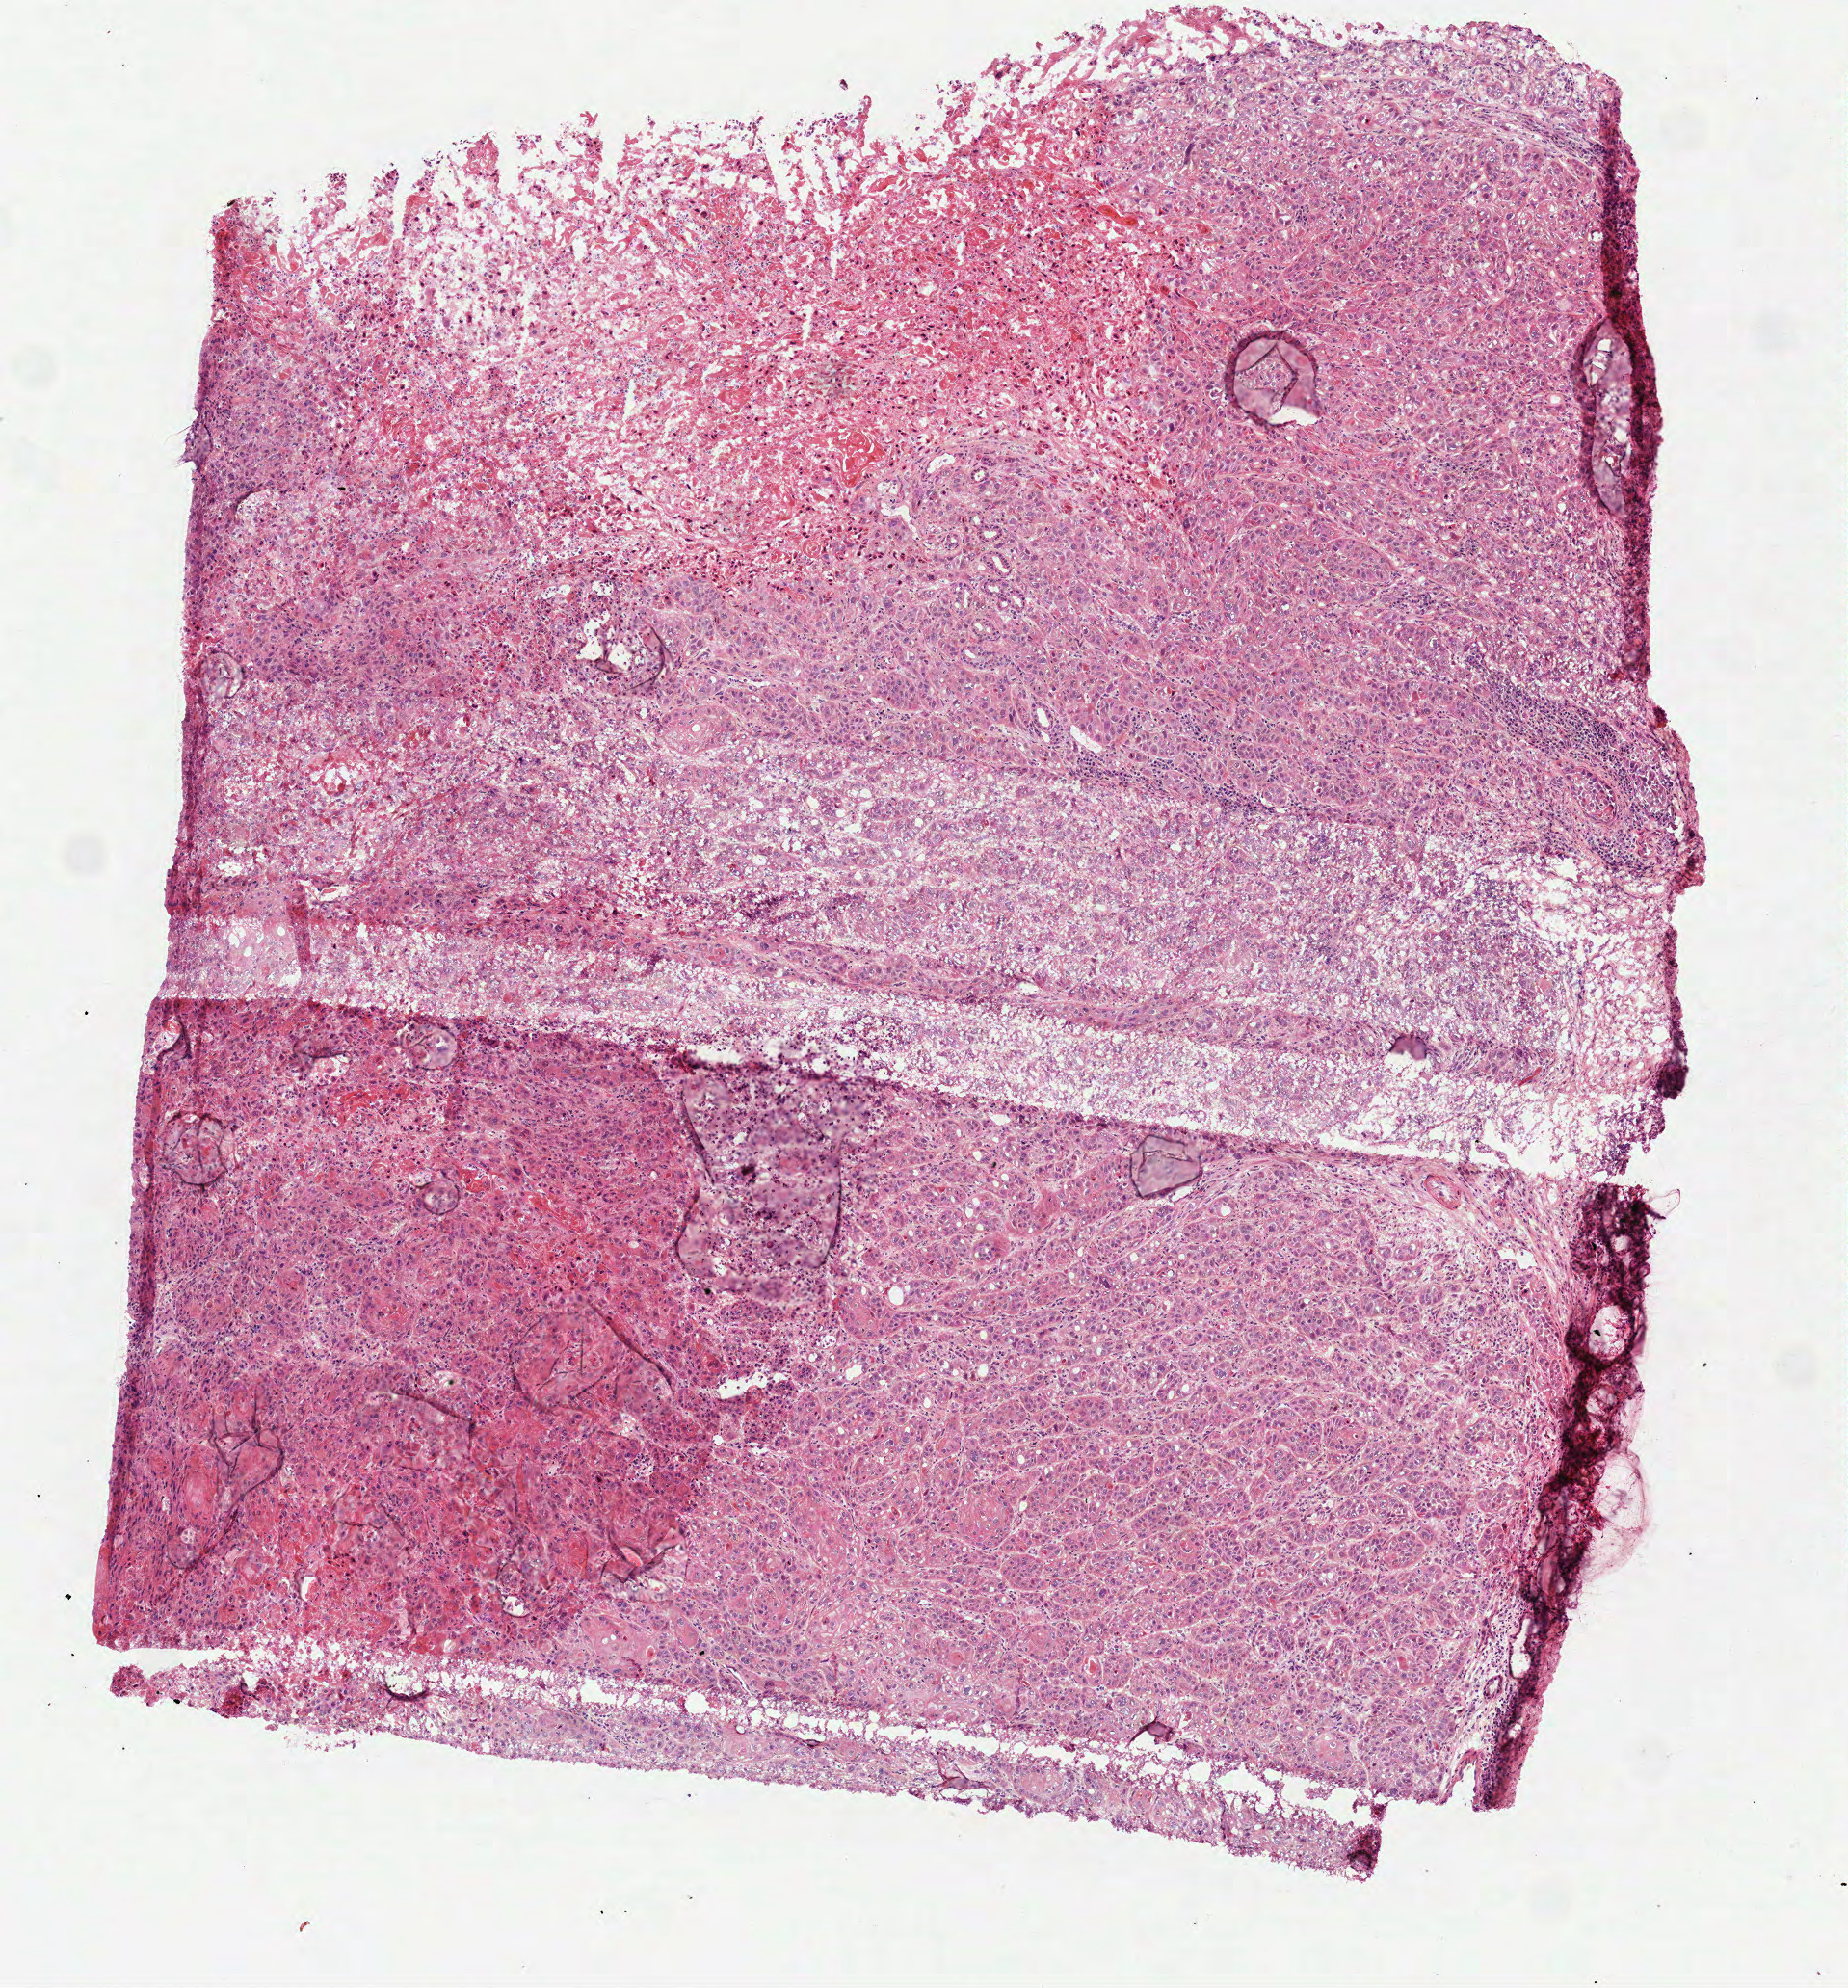
Whole-slide histology image, H&E-stained, low-resolution overview of the scanned area, about 3.9 x 4.2 mm (from a 40x scan). Frozen section from the top of the tissue portion. Primary tumour sample from the head and neck. Female, age 64 years at initial diagnosis. Histologic grade: G2 (moderately differentiated). Composition of this section per pathologist review: tumour cells 82%, tumour nuclei 80%, normal cells 0%, stromal cells 10%, necrosis 8%.
- diagnosis: Squamous cell carcinoma, NOS (larynx, NOS)
- laterality: midline
- TNM: T4a N2b
- AJCC pathologic stage: IVA (7th edition)